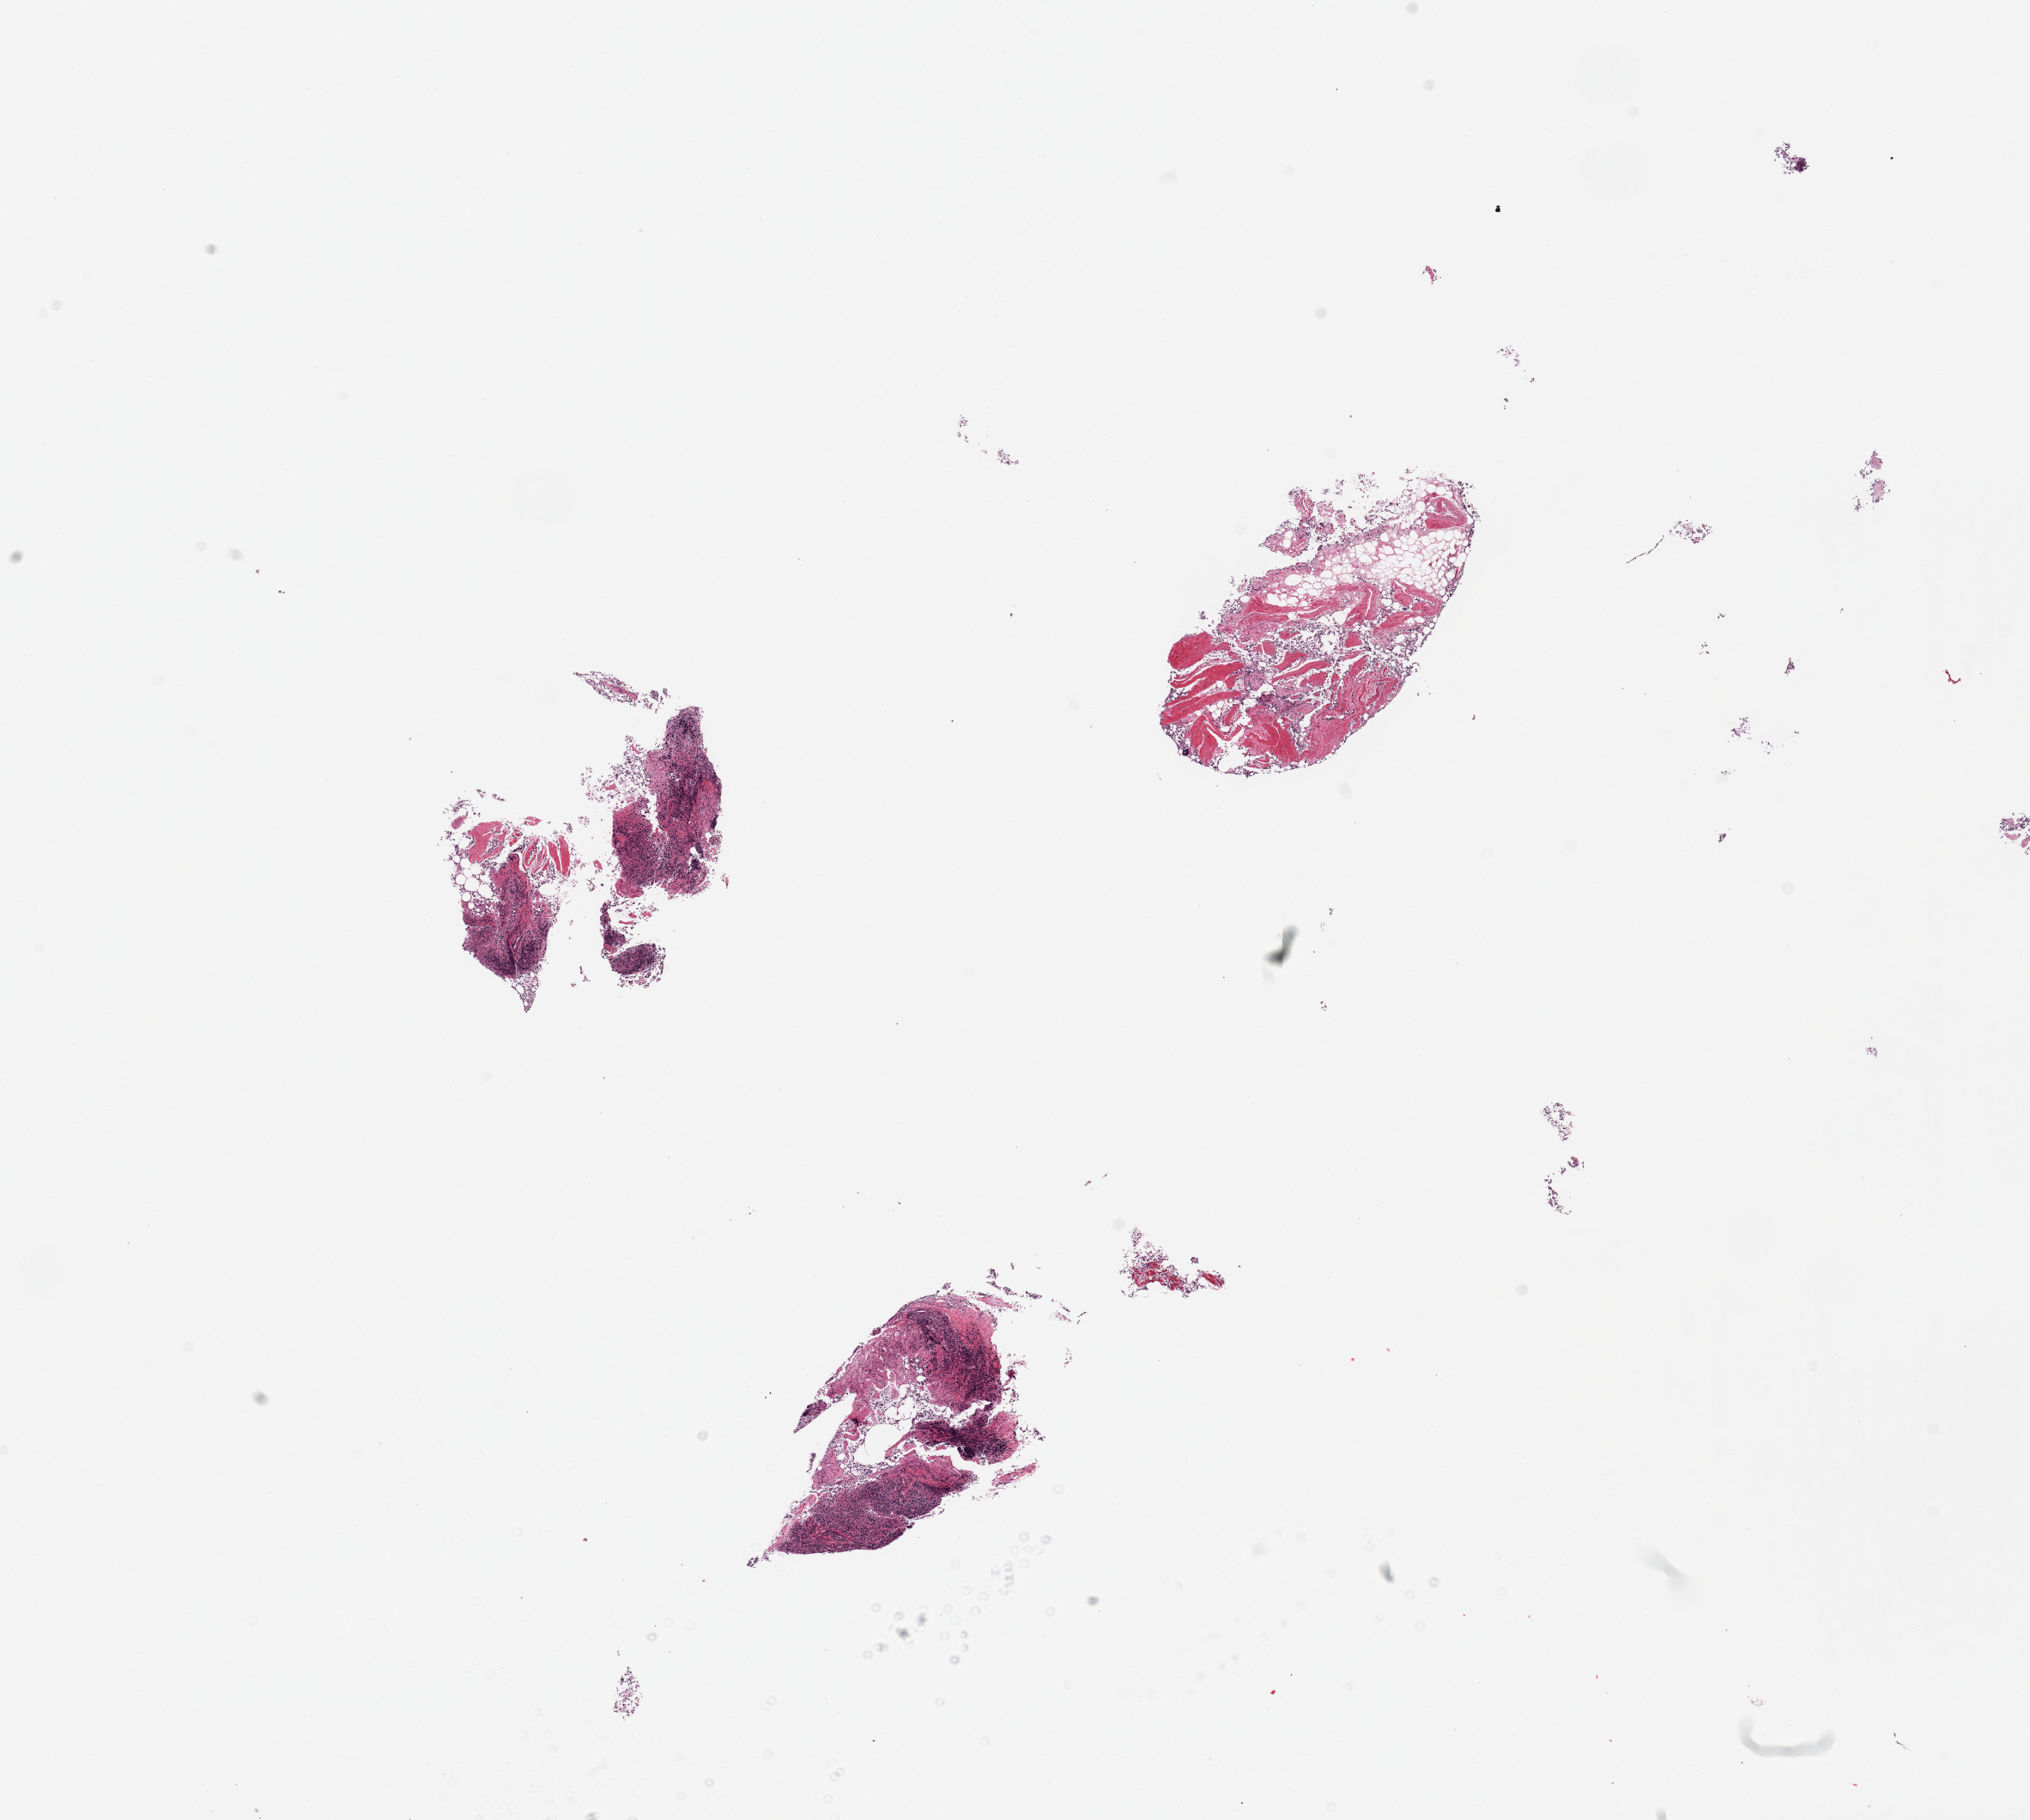
Whole-slide image, H&E stain, a low-resolution overview of the entire scanned area, about 18.7 x 16.8 mm (from a 20x scan); PAXgene-fixed paraffin-embedded (PFPE) section; section of ileum (target tissue); donor tissue sample. Donor: male.
- reviewer comment on this tissue sample: 3 pieces; fragments of autolyzed mucosa with lymphoid component and smooth muscle